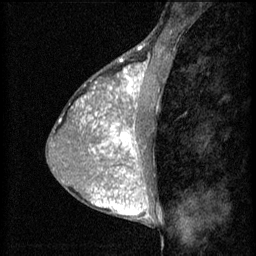
Breast MRI (dynamic contrast-enhanced), one sagittal slice. Position 29 of 60 along the scan axis. 3 images stored at this slice position (order not interpretable as contrast timing). 1.5 T. TE 4.2 ms, TR 8.2 ms. 2 mm slice thickness. 256 × 256 image matrix, field of view 180 × 180 mm. Female patient, age 38 years.
Structures marked on this image (semi-automatically segmented with operator editing):
- analysis volume of interest (the breast-tissue region the enhancement analysis was run in; not a lesion): bounding box <95,106,156,171> (left, top, right, bottom; pixels)
- tumour enhancement mask (voxels above the 70 % enhancement threshold inside the analysis volume of interest): <95,106,146,171>